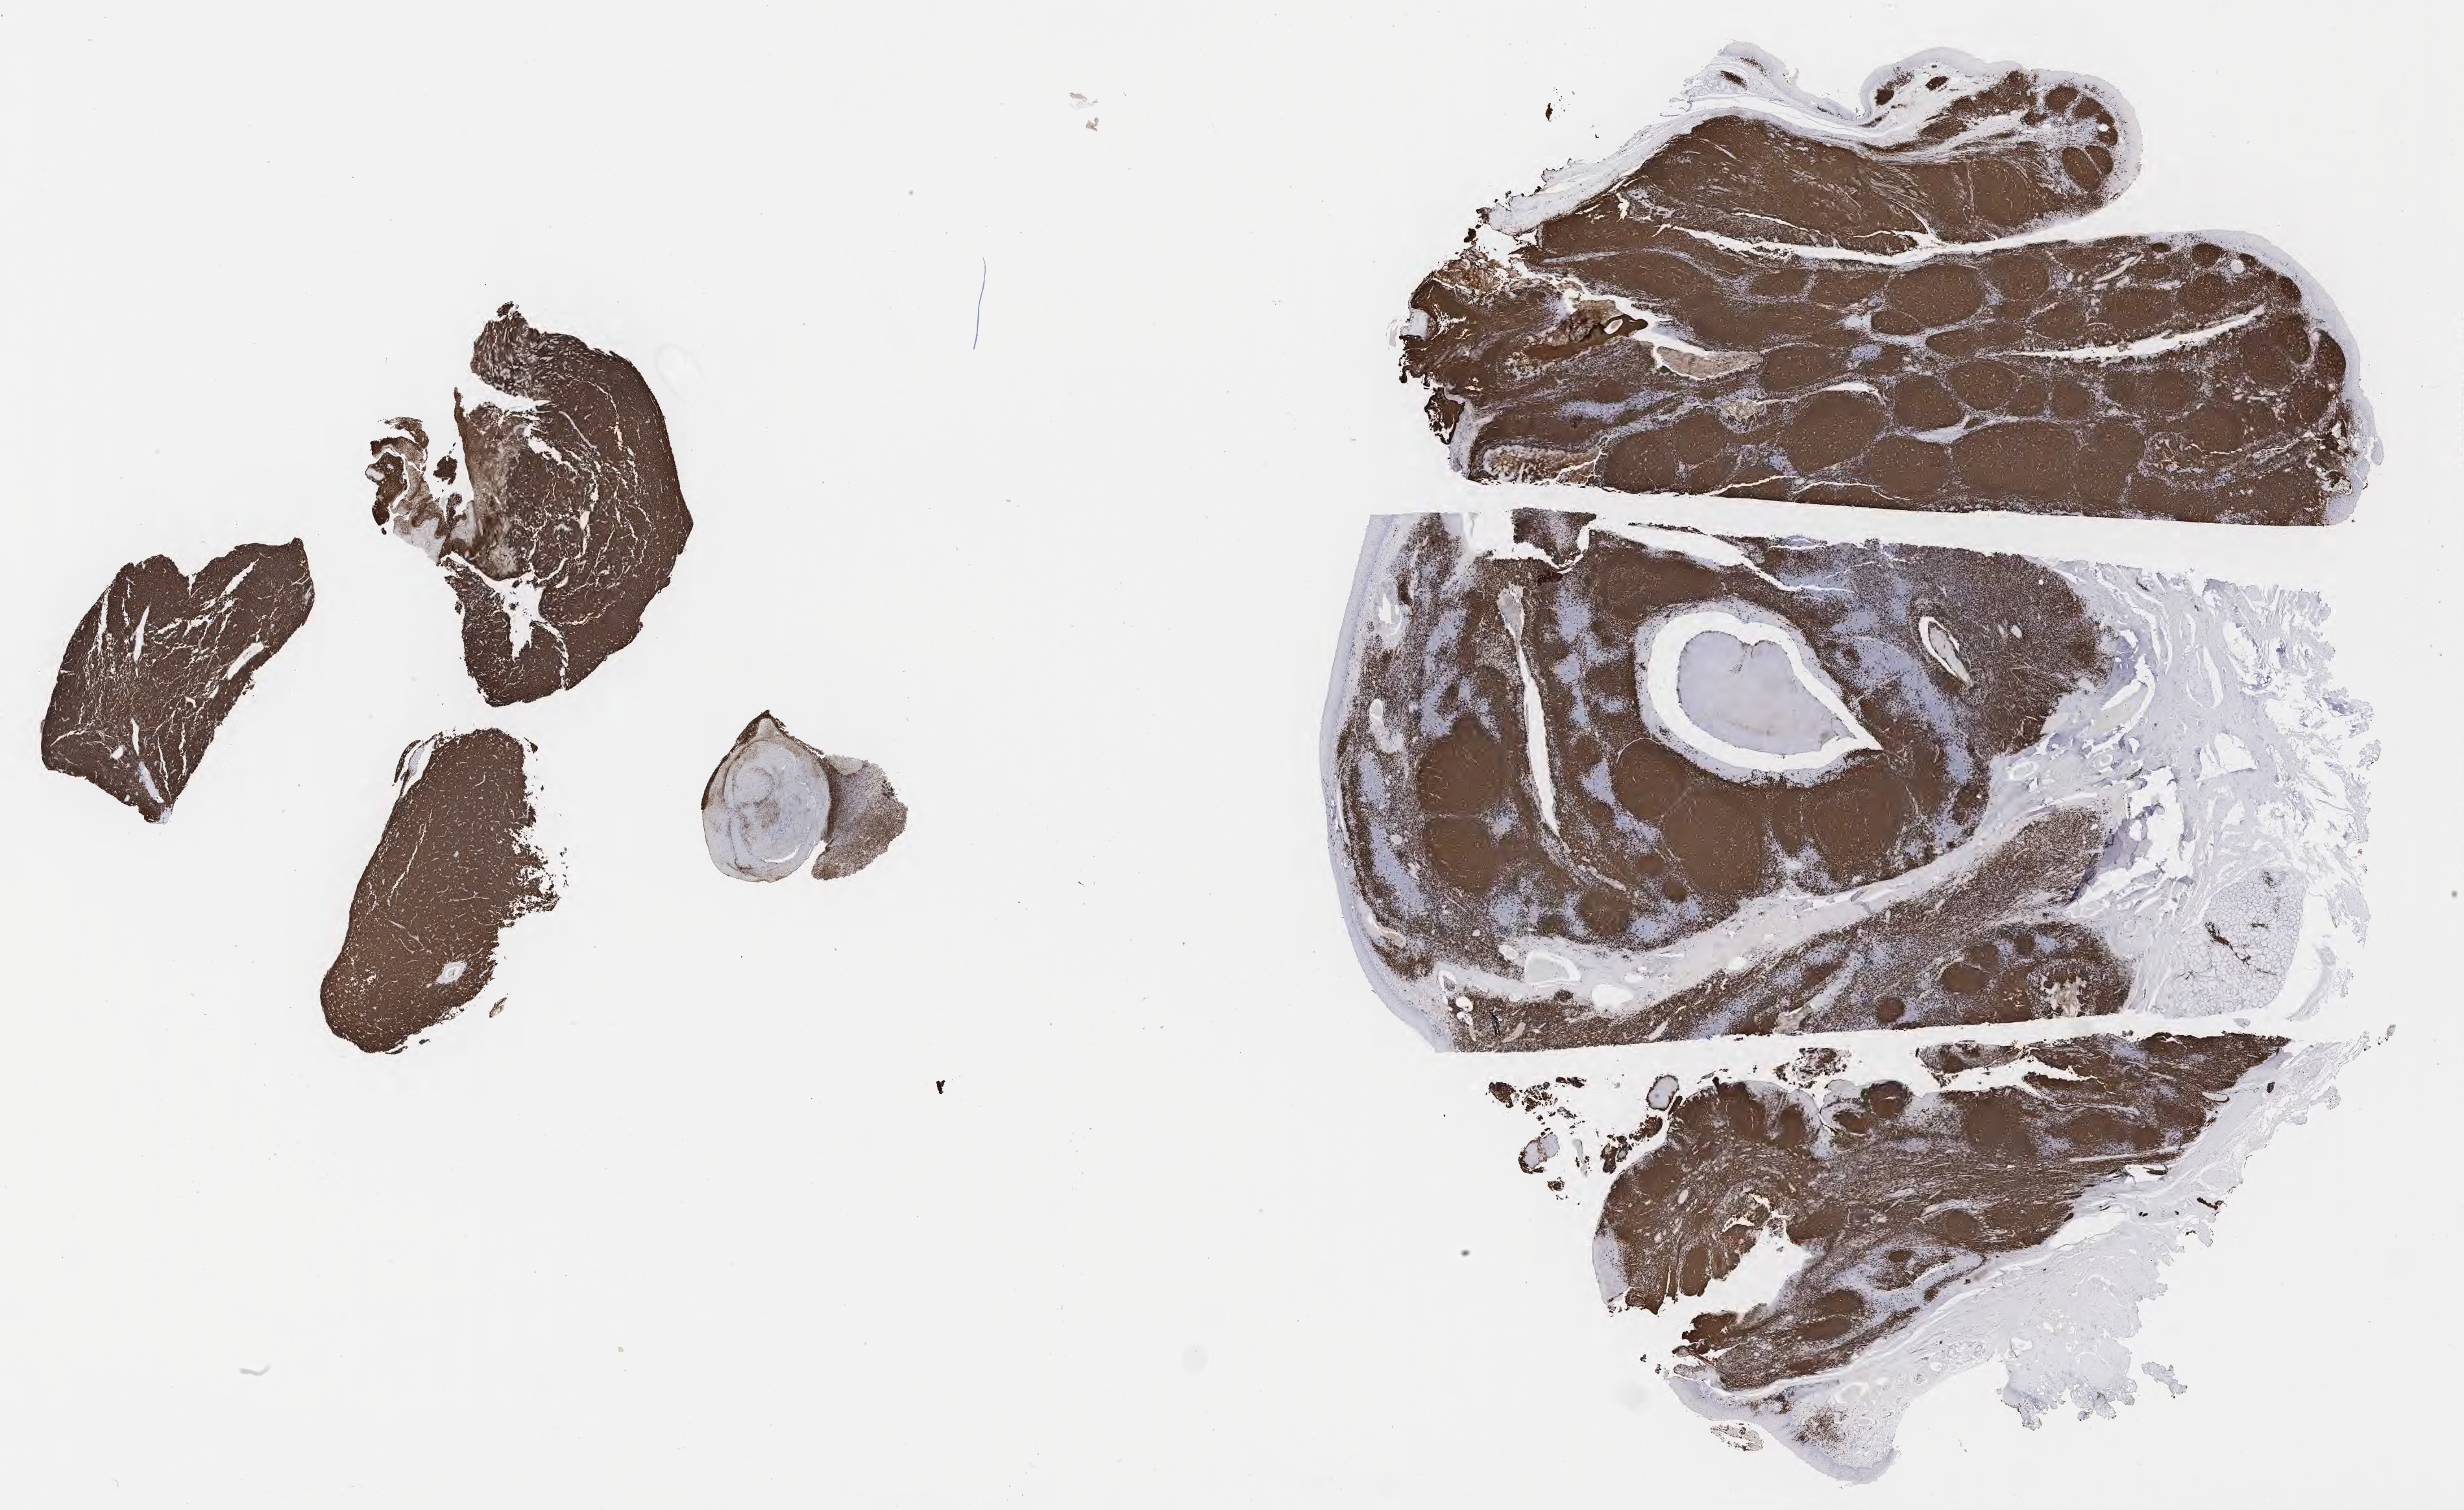
Whole-slide image, immunohistochemical stain for CD20 — whole scanned area (about 30.7 x 18.8 mm) shown as a low-resolution overview. Tumor tissue. Patient male; 10 years old.
* diagnosis: Burkitt lymphoma, NOS